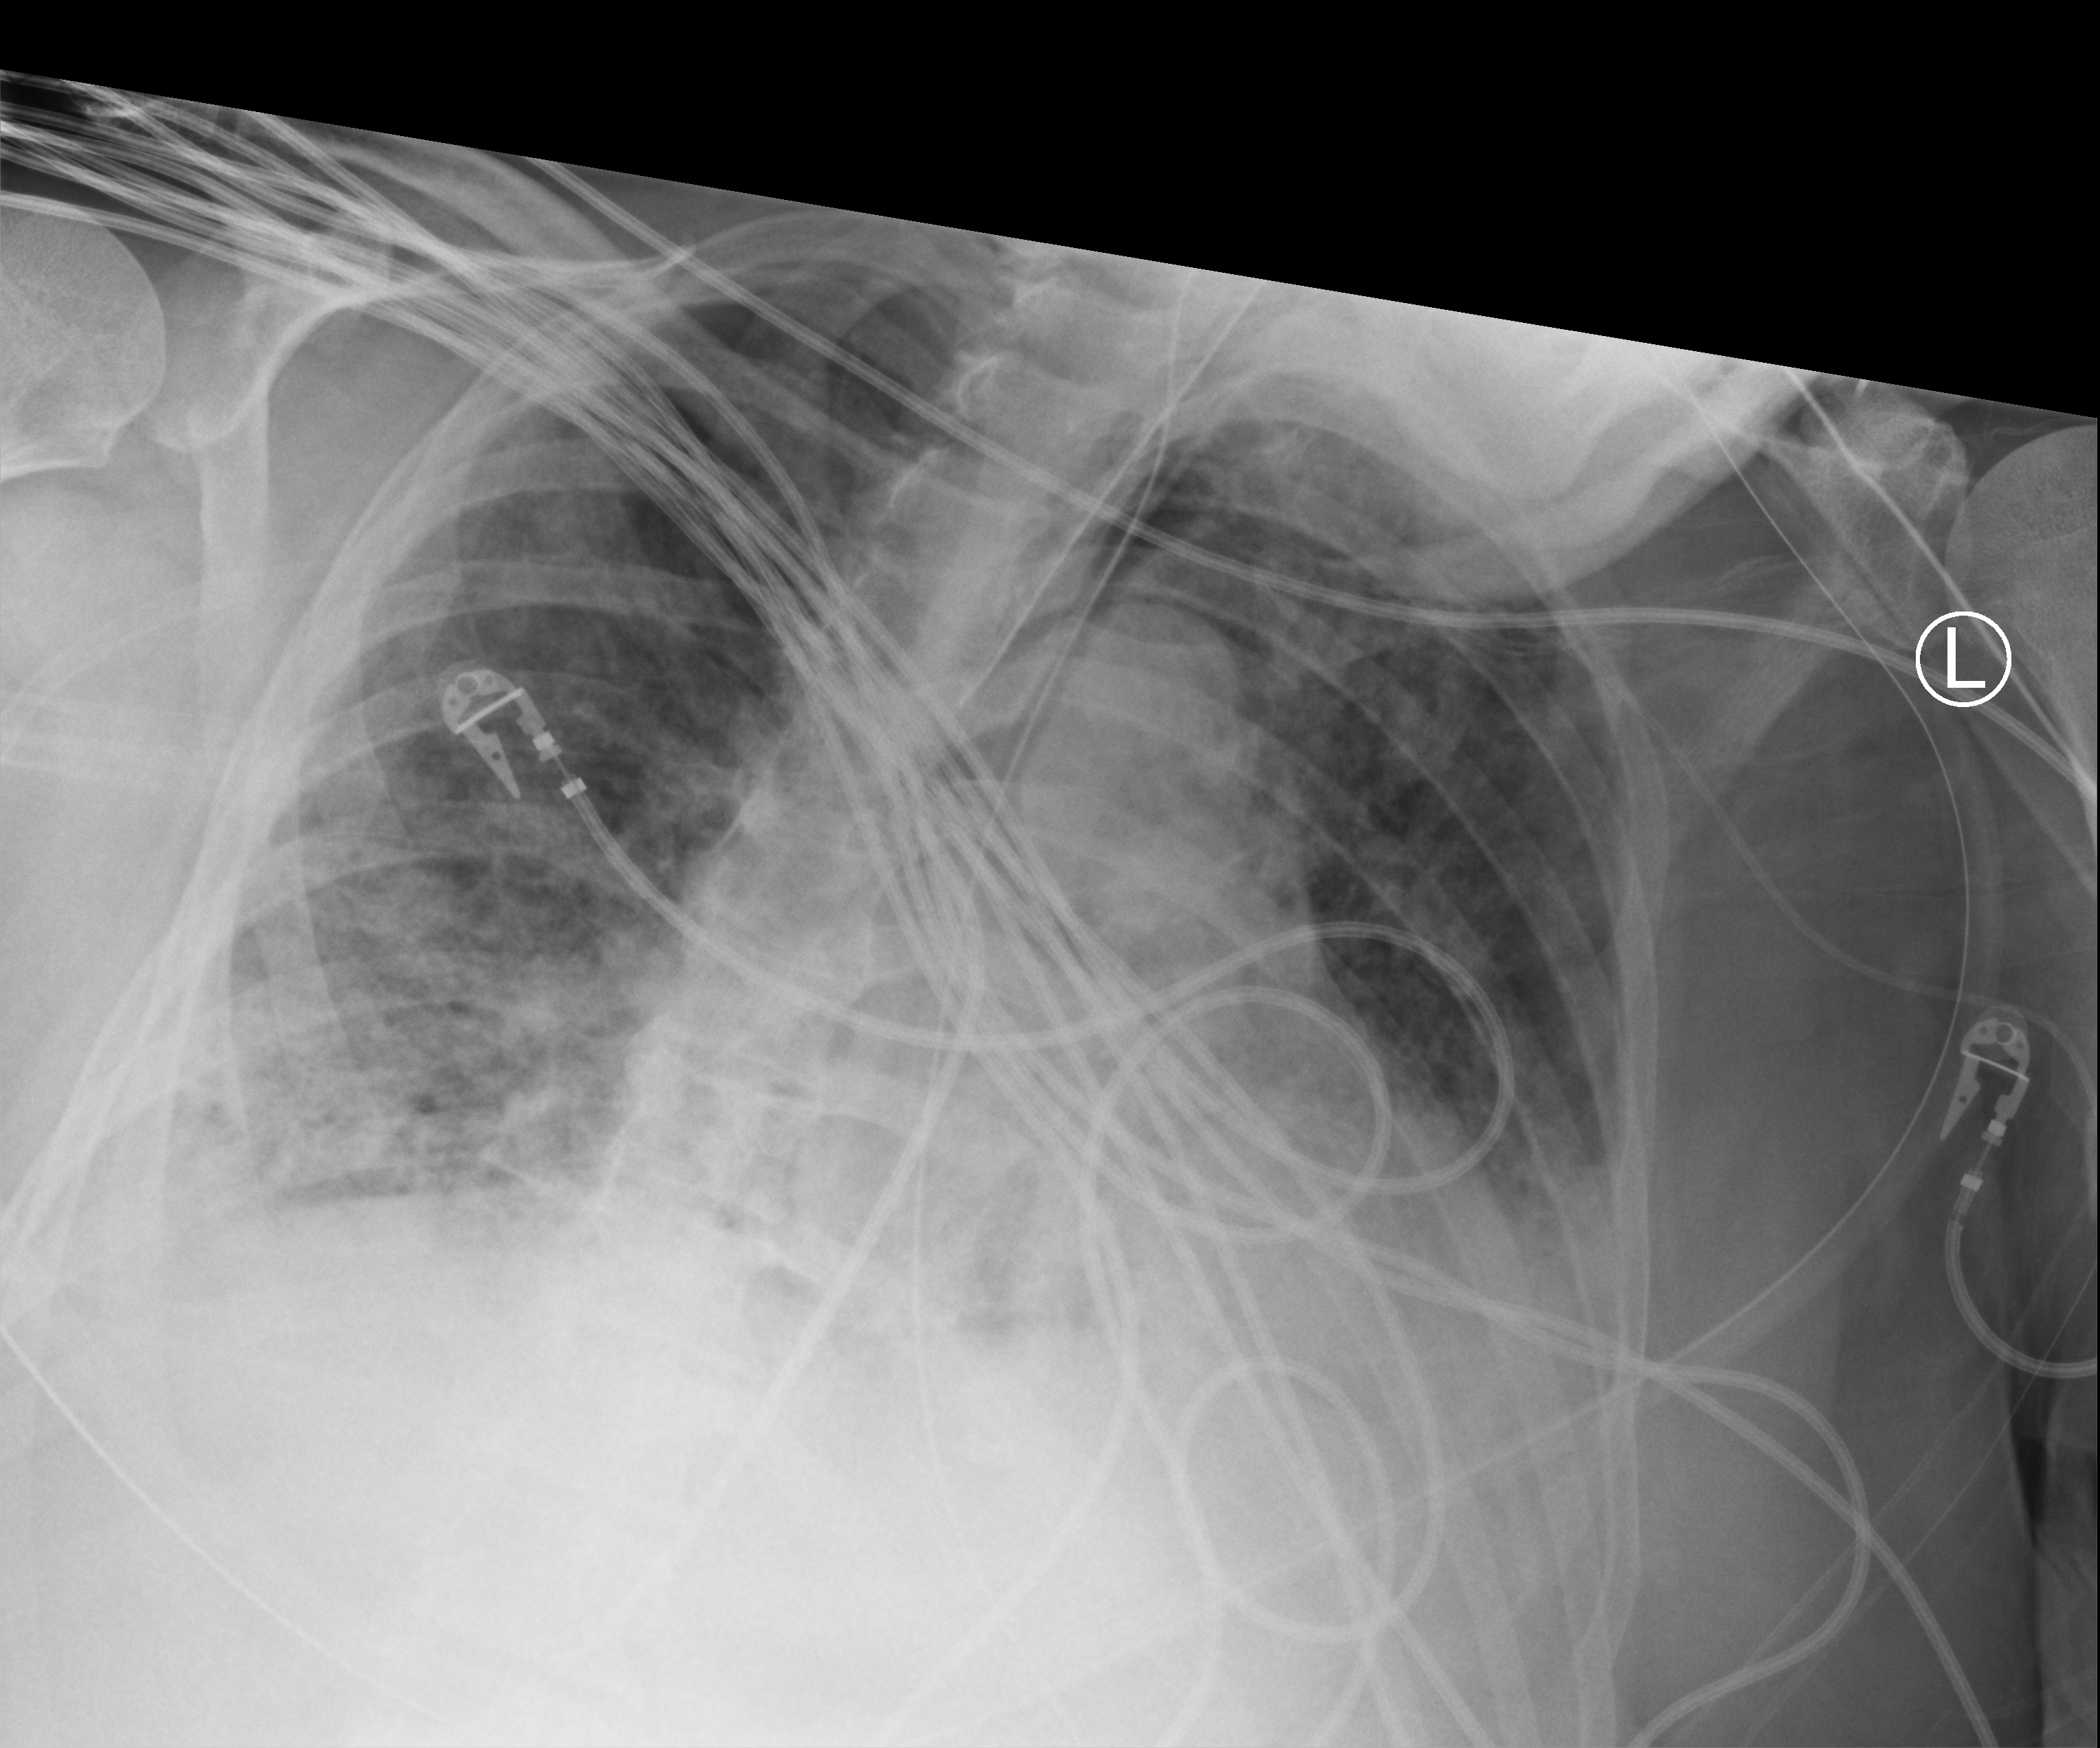
Portable chest radiograph; anteroposterior (AP) projection. Patient hospitalised with COVID-19; male, aged 60–74 years.
Admission-level facts for this patient (not findings on this image; timing relative to this image not recorded): mechanically ventilated during this hospital stay: yes.